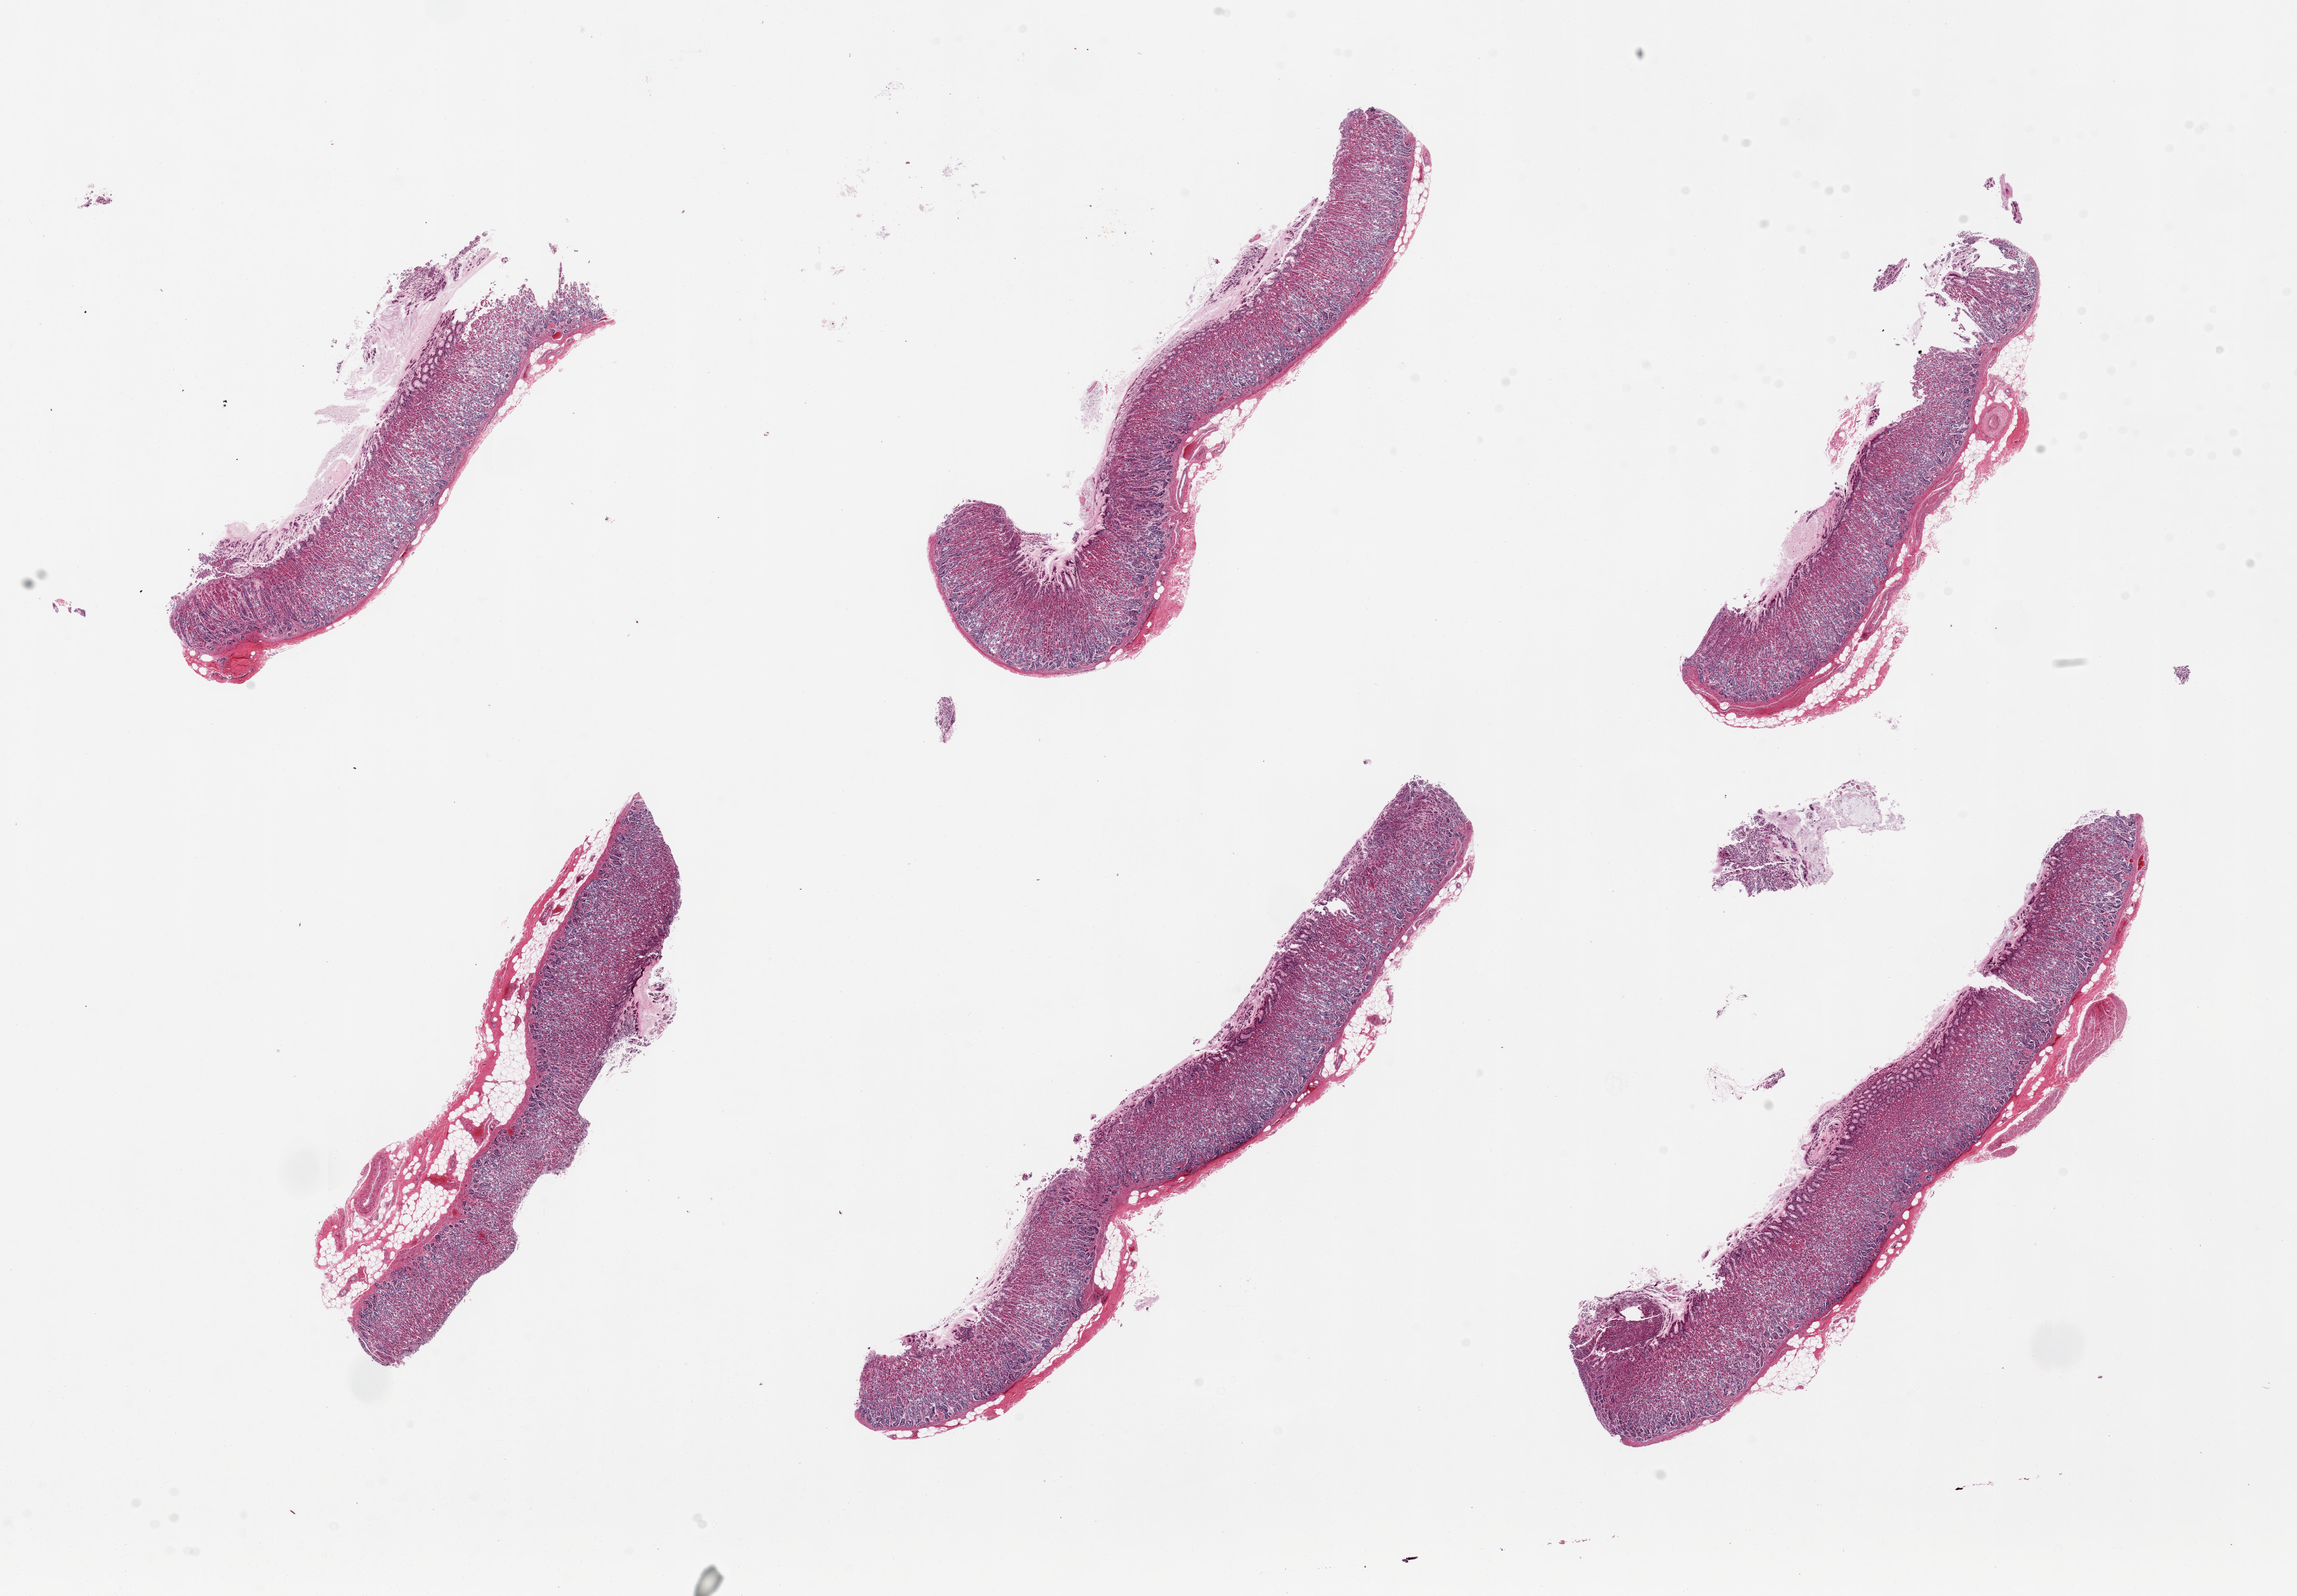
Digitized haematoxylin and eosin-stained section, shown as a low-resolution overview of the whole scanned area (about 27.6 x 19.2 mm, from a 20x scan), PAXgene-fixed paraffin-embedded (PFPE) section, section of stomach (target tissue), donor tissue sample. Donor: female.
Pathologist's review note for this sample: 6 pieces, up to 10x2mm; mucosa is 90--100% of thickness, remarkably pure but moderately autolyzed.